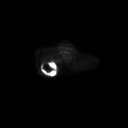
FDG PET of an extremity soft-tissue mass (from a PET/CT study), one axial slice. 128 × 128 image matrix. Patient: male, 61 years. Case-level facts recorded for this patient, not image findings: histological type: pleiomorphic spindle cell undifferentiated; grade: high; site of the primary tumour: right parascapusular.
Structures marked on this image (expert contour drawn on MRI and transferred to this co-registered scan by the dataset authors):
- gross tumour volume including surrounding oedema: box from (x=40, y=61) to (x=60, y=75) px
- gross tumour volume (mass): (x=41, y=62)–(x=55, y=75)